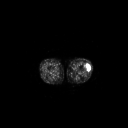
FDG PET of an extremity soft-tissue mass (from a PET/CT study), one axial slice. Slice 178 of 223 in the series (ordered by position). 3.27 mm slice thickness. 128 × 128 image matrix, field of view 700 × 700 mm. Patient: female, 16 years. Case-level facts recorded for this patient, not image findings: histological type: spindle cell suggestive of biphasic synovial sarcoma; grade: intermediate; site of the primary tumour: left knee.
Structures marked on this image (expert contour drawn on MRI and transferred to this co-registered scan by the dataset authors):
- gross tumour volume including surrounding oedema: bounding box <85,62,91,71> (left, top, right, bottom; pixels)
- gross tumour volume (mass): <85,62,91,71>